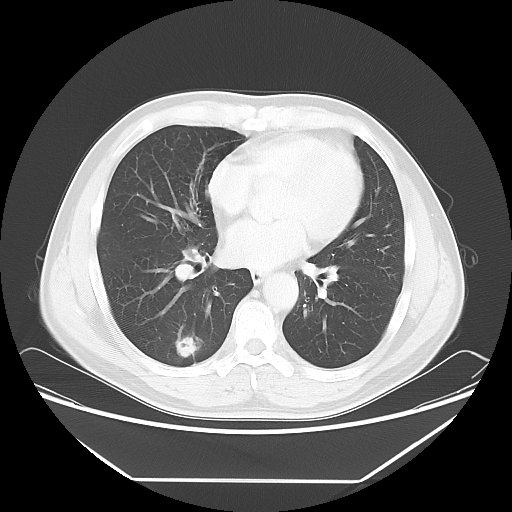
Chest CT, one axial slice. Slice 30 of 65 in the series (ordered by position). Reconstruction kernel LUNG. 120 kVp. Lung window (W 1500 / L -600 HU). 512 × 512 image matrix, field of view 418 × 418 mm. Male patient, age 50 years. Case-level facts recorded for this patient, not image findings: clinical TNM (as recorded): T1c N0 M0; histopathological grade: G3.
Annotated regions visible in this slice (bounding box drawn by a radiologist):
- lung tumour (recorded histology: adenocarcinoma): bounding box (x1, y1, x2, y2) in pixels: (171, 332, 207, 363)